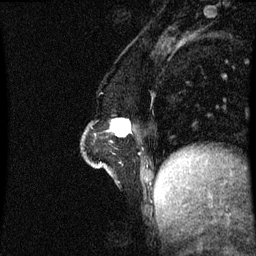
Breast MRI (dynamic contrast-enhanced), one sagittal slice. Position 19 of 60 along the scan axis. Dynamic contrast-enhanced series, image 2 of 3 at this slice position (ordered by acquisition). 1.5 T. TE 4.2 ms, TR 8.9 ms. 2.1 mm slice thickness. 256 × 256 image matrix, field of view 200 × 200 mm. Patient: female, 47 years. Case-level facts recorded for this patient, not image findings: setting: breast cancer imaged before/during neoadjuvant chemotherapy; receptor status: HR-positive, HER2-negative.
Annotated regions visible in this slice (semi-automatic segmentation, software-assisted and operator-edited):
- analysis volume of interest (the breast-tissue region the enhancement analysis was run in; not a lesion): box from (x=83, y=120) to (x=131, y=163) px
- tumour enhancement mask (voxels above the 70 % enhancement threshold inside the analysis volume of interest): (x=113, y=120)–(x=131, y=137)